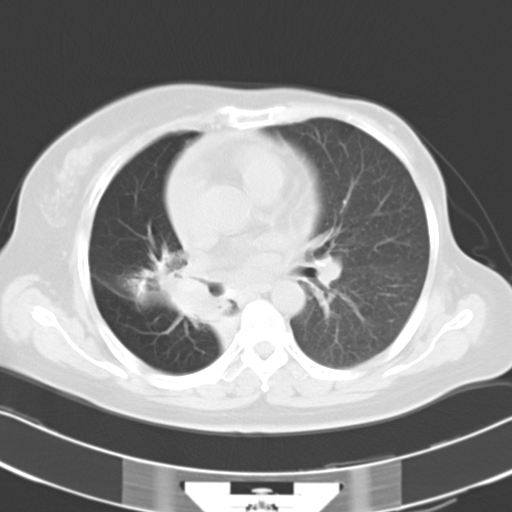
Chest CT, one axial slice. Position 17 of 30 along the scan axis. Reconstruction kernel B40f. 120 kVp. Lung window (W 1500 / L -600 HU). 8 mm slice thickness. 512 × 512 image matrix, field of view 331 × 331 mm. Female patient, age 53 years. Case-level facts recorded for this patient, not image findings: clinical TNM (as recorded): T2b N1 M0.
Structures marked on this image (rectangle marked by the reading radiologist):
- lung tumour (recorded histology: adenocarcinoma): box from (x=139, y=253) to (x=234, y=322) px